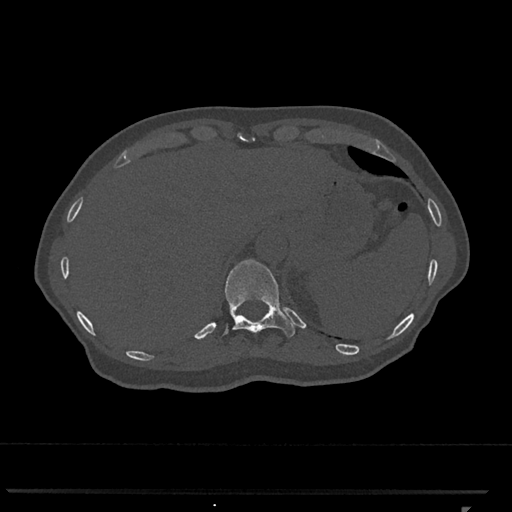
CT including the spine, one axial slice. Position 520 of 793 along the scan axis. Reconstruction kernel Br40s/3. Bone window (W 1800 / L 400 HU). 0.5 mm slice thickness. 512 × 512 image matrix. Patient: female, 62 years. Case-level facts recorded for this patient, not image findings: primary cancer: renal.
Outlined on this slice (semi-automatically segmented with operator editing):
- T11 vertebra: bounding box <225,259,295,338> (left, top, right, bottom; pixels)